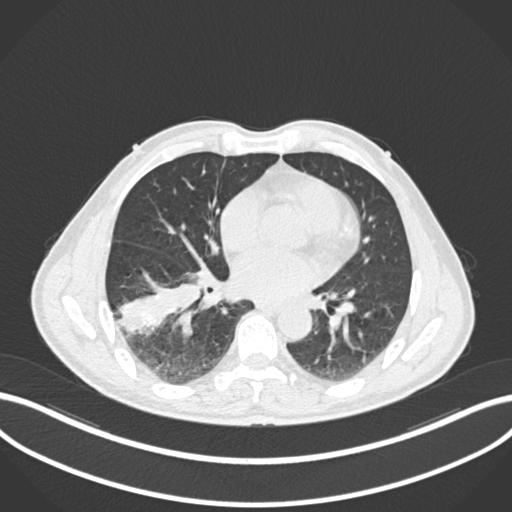
Chest CT, one axial slice; slice 85 of 208 in the series (ordered by position); lung window (W 1500 / L -600 HU); 512 × 512 image matrix, field of view 400 × 400 mm. Male patient, age 58 years. Case-level facts recorded for this patient, not image findings: clinical TNM (as recorded): T3 N0 M0.
Structures marked on this image (bounding box drawn by a radiologist):
- lung tumour (recorded histology: squamous cell carcinoma): box from (x=107, y=275) to (x=198, y=343) px